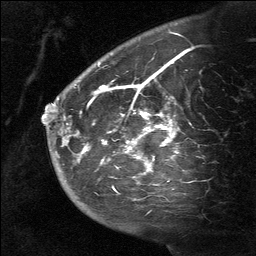
Breast MRI (dynamic contrast-enhanced), one sagittal slice; slice 46 of 64 in the series (ordered by position); dynamic contrast-enhanced study with each time point stored as its own series, time point 2 of 3 at this slice position (early post-contrast, ordered by acquisition time); 1.5 T; TE 4.8 ms, TR 27 ms; 256 × 256 image matrix. Patient: female, 39 years. From the clinical record (not read from this slice): setting: breast cancer imaged before/during neoadjuvant chemotherapy; receptor status: HER2-positive.
Annotated regions visible in this slice (semi-automatic segmentation, software-assisted and operator-edited):
- analysis volume of interest (the breast-tissue region the enhancement analysis was run in; not a lesion): box from (x=58, y=40) to (x=201, y=217) px
- tumour enhancement mask (voxels above the 90 % enhancement threshold inside the analysis volume of interest): (x=84, y=85)–(x=179, y=174)